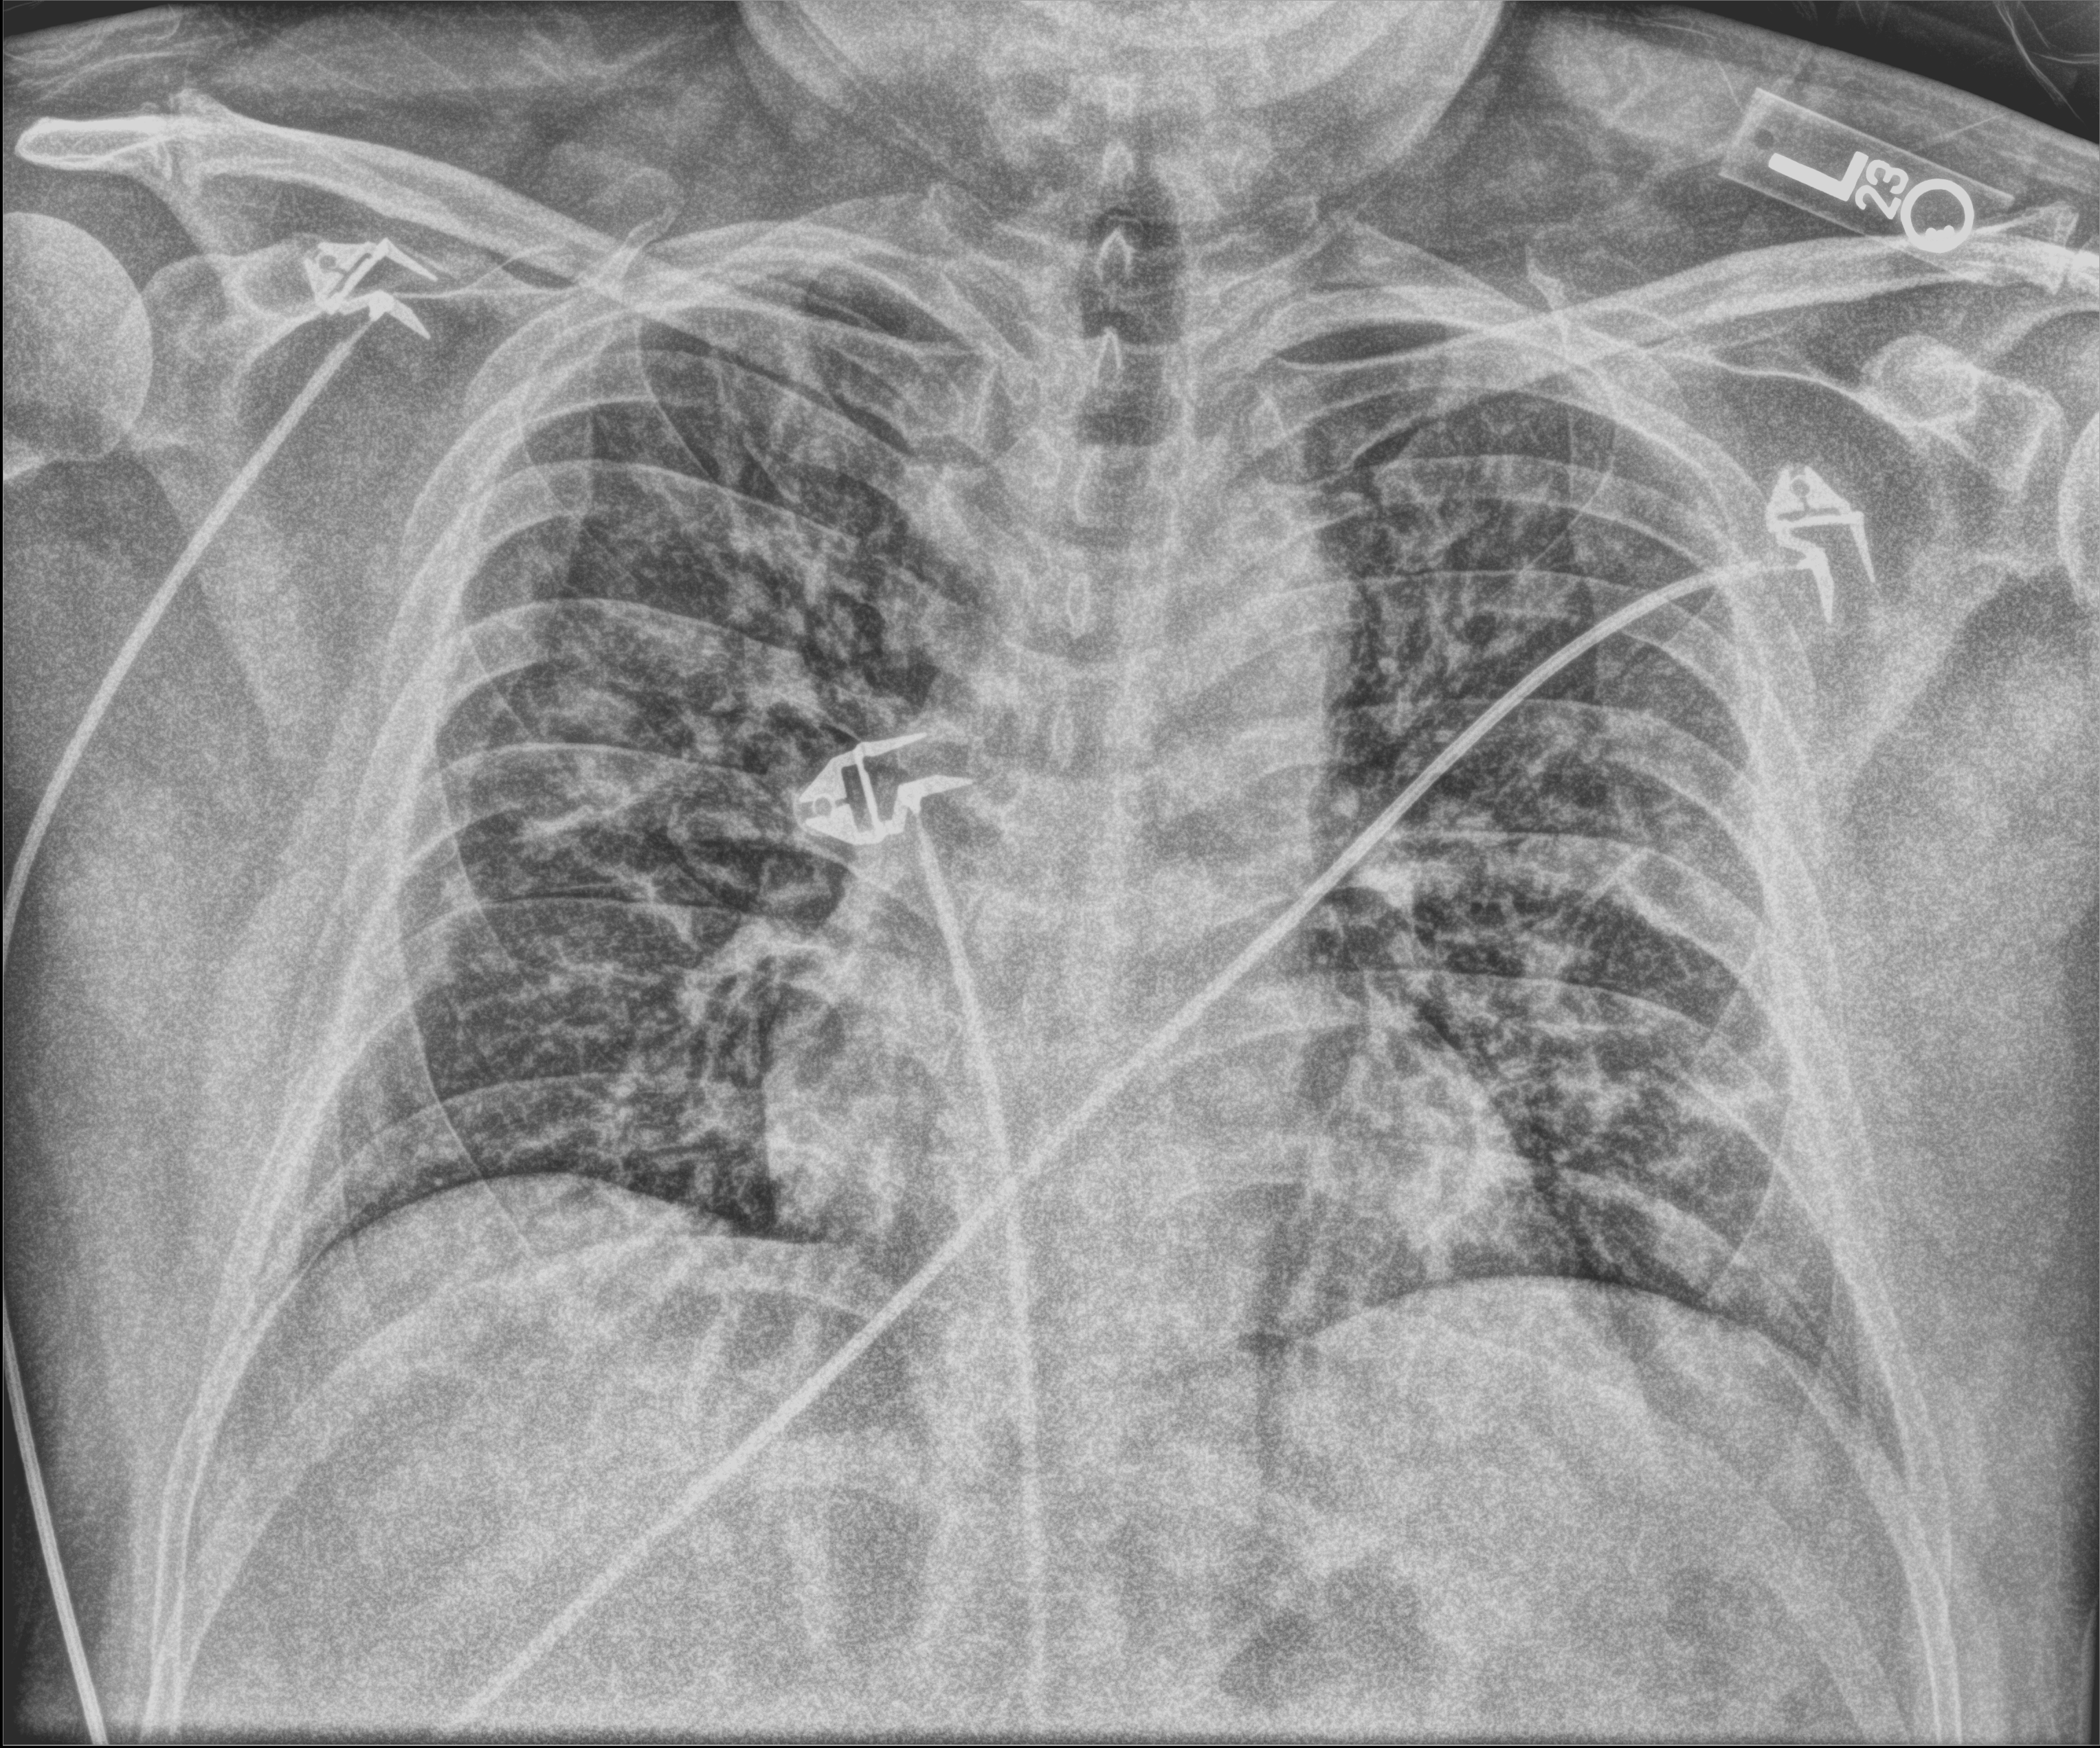
Portable chest radiograph, anteroposterior (AP) projection. Patient hospitalised with COVID-19; male, aged 18–59 years.
Admission-level facts for this patient (not findings on this image; timing relative to this image not recorded):
- hypertension (admission record): no
- admitted to intensive care during this hospital stay: no
- smoking status (admission record): former